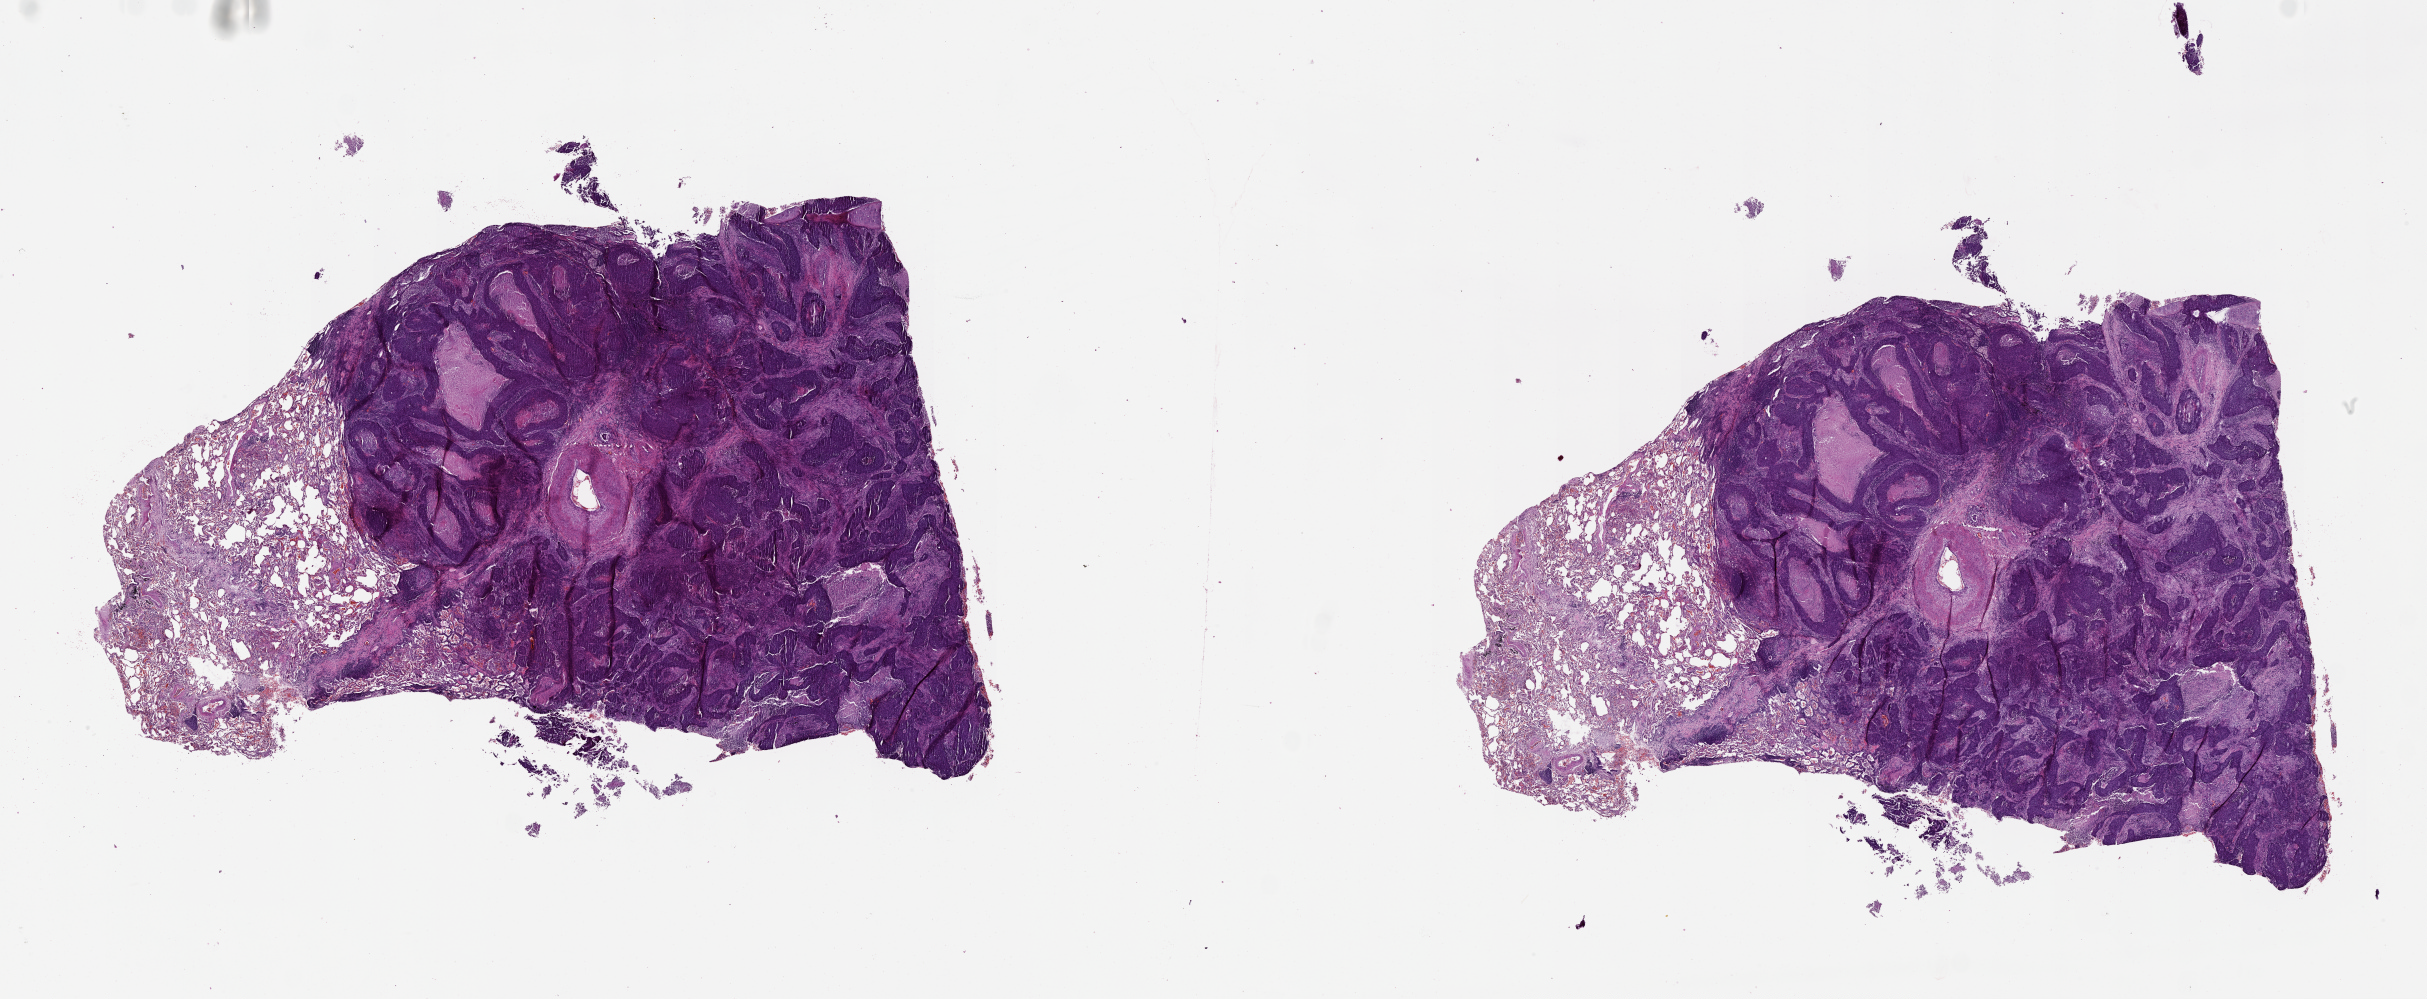
Digitized H&E tissue section (whole slide), a low-resolution overview of the entire scanned area, about 39.1 x 16.1 mm (acquisition: 20x scan). Tumour tissue sample, lung. Female, 62 y/o.
- patient diagnosis (cohort enrolment): squamous cell carcinoma (lung)